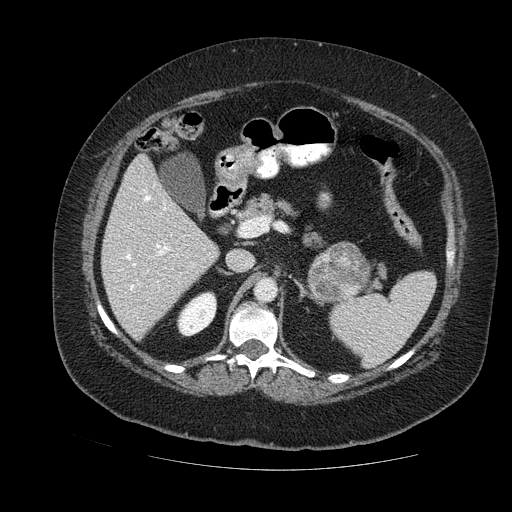
Contrast-enhanced abdominal CT, one axial slice. Slice 71 of 121 in the series (ordered by position). Soft-tissue window (W 400 / L 40 HU). 2.5 mm slice thickness. 512 × 512 image matrix. Female patient. From the clinical record (not read from this slice): diagnosis: adrenocortical carcinoma; tumour side: left adrenal.
Outlined on this slice (semi-automatically segmented with operator editing):
- mass: bounding box [x1, y1, x2, y2] px = [307, 243, 371, 299]